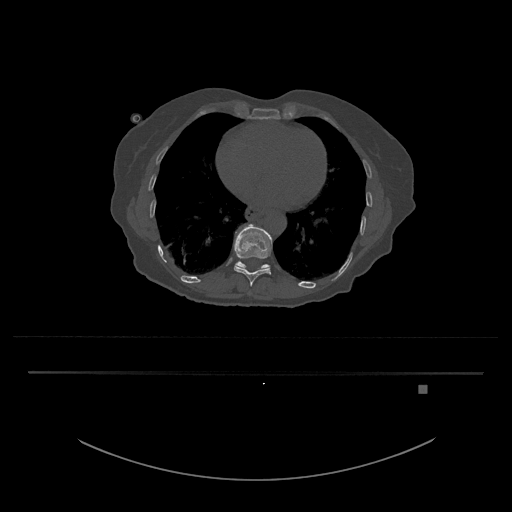
CT including the spine, one axial slice; slice 702 of 797 in the series (ordered by position); reconstruction kernel Br40s/3; bone window (W 1800 / L 400 HU); 0.5 mm slice thickness; 512 × 512 image matrix, field of view 500 × 500 mm. Female patient, age 57 years. From the clinical record (not read from this slice): primary cancer: cervical.
Annotated regions visible in this slice (semi-automatic segmentation, software-assisted and operator-edited):
- T10 vertebra: bounding box <233,225,272,287> (left, top, right, bottom; pixels)
- T11 vertebra: <235,261,271,270>